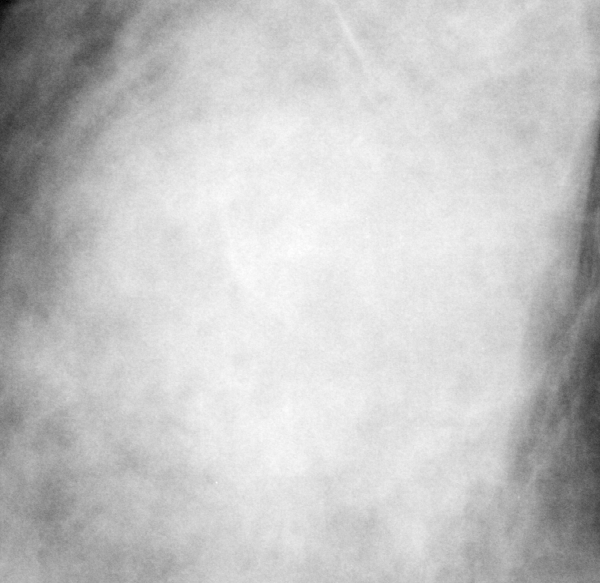
Crop from a digitized film mammogram around one marked abnormality, right breast, CC view.
- Finding: mass, shape round, margins ill defined; BI-RADS assessment category 4; pathology (as recorded): malignant.